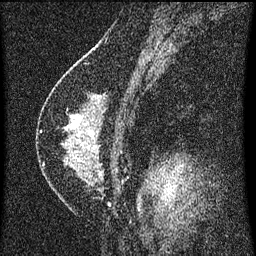
Breast MRI (dynamic contrast-enhanced), one sagittal slice; slice 38 of 60 in the series (ordered by position); dynamic contrast-enhanced series, image 2 of 3 at this slice position (ordered by acquisition); 1.5 T; TE 4.2 ms, TR 8 ms; 2 mm slice thickness; 256 × 256 image matrix, field of view 180 × 180 mm. Female patient, age 47 years.
Structures marked on this image (semi-automatically segmented with operator editing):
- analysis volume of interest (the breast-tissue region the enhancement analysis was run in; not a lesion): box from (x=42, y=92) to (x=130, y=199) px
- tumour enhancement mask (voxels above the 70 % enhancement threshold inside the analysis volume of interest): (x=71, y=116)–(x=81, y=129)